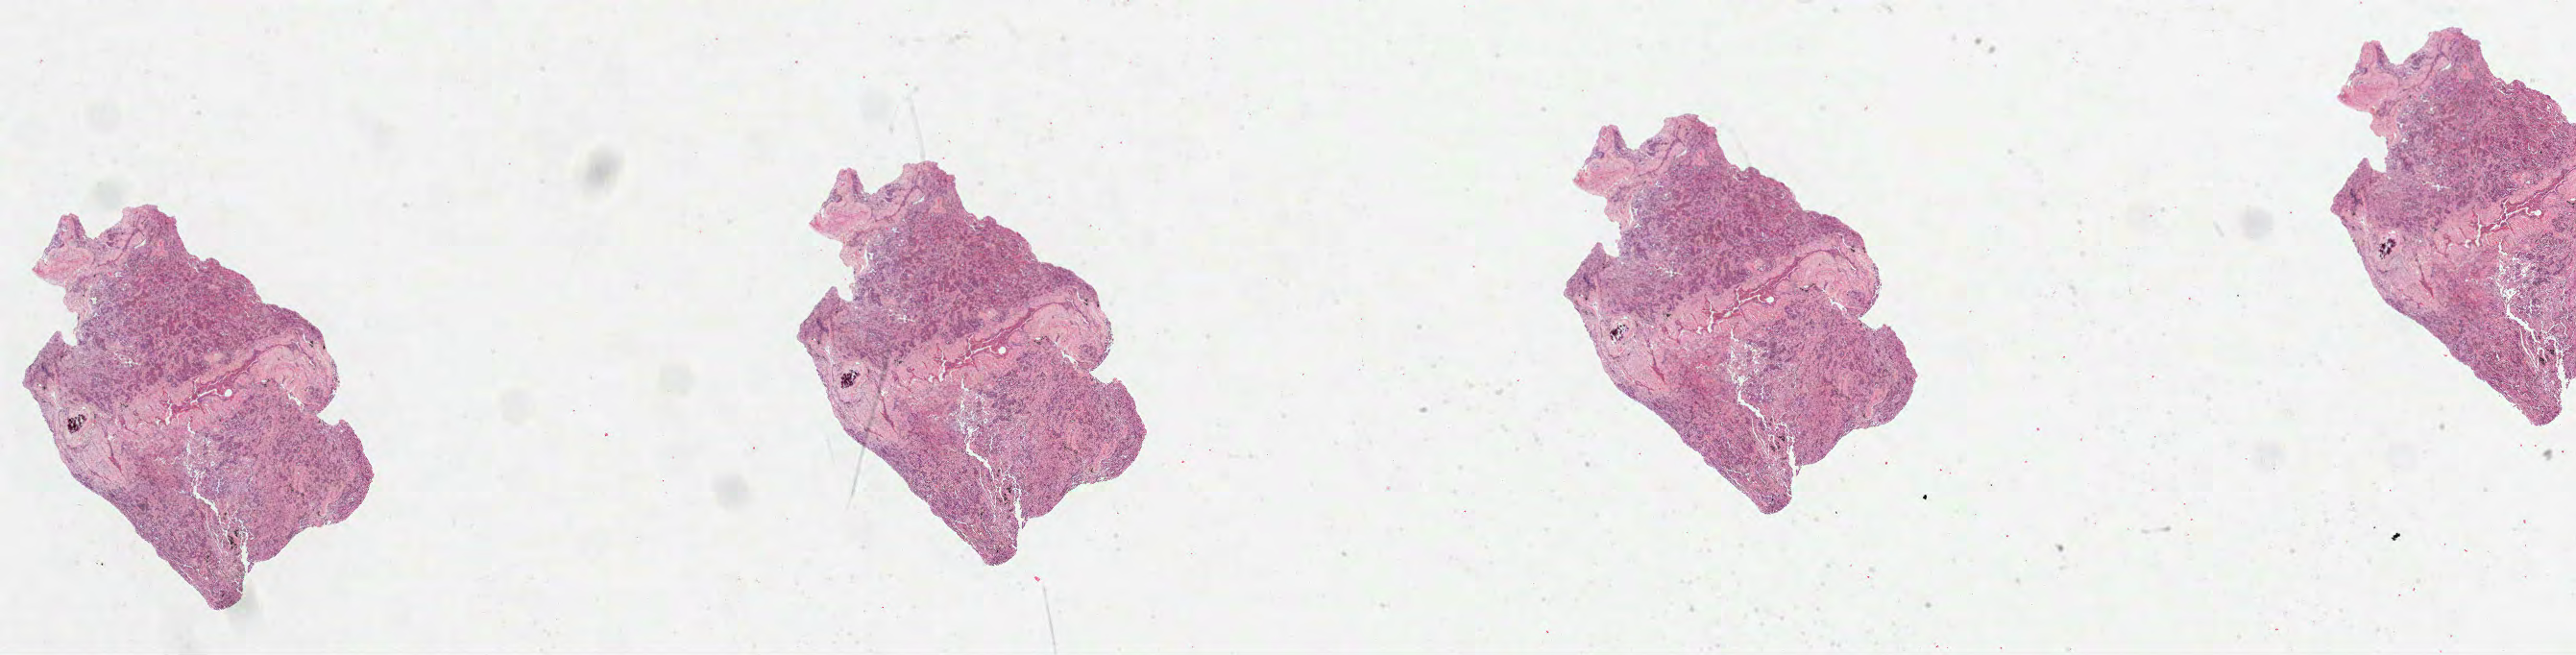
H&E-stained whole-slide image — low-resolution overview of the scanned area, about 43.3 x 11.0 mm. Formalin-fixed paraffin-embedded (FFPE) diagnostic section. Sample: primary tumour, lung. Patient: male, age at initial diagnosis 68 years.
• diagnosis: Adenocarcinoma, NOS (lower lobe, lung)
• laterality: right